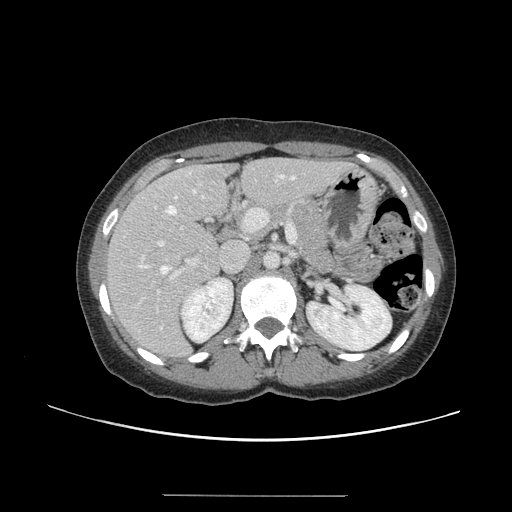
Contrast-enhanced abdominal CT, one axial slice; position 79 of 144 along the scan axis; 120 kVp; soft-tissue window (W 400 / L 40 HU); 512 × 512 image matrix, field of view 380 × 380 mm. Female patient, age 53 years. From the clinical record (not read from this slice): diagnosis: colorectal cancer liver metastases, imaged before liver resection; multiple liver metastases: yes; largest metastasis: 1.1 cm; disease in both lobes: no.
Outlined on this slice (expert manual segmentation):
- hepatic veins: bounding box [x1, y1, x2, y2] px = [161, 175, 295, 274]
- liver: [107, 159, 345, 358]
- planned liver remnant (the part of the liver to remain after resection): [108, 159, 317, 299]
- portal vein (with intrahepatic branches): [138, 203, 297, 294]